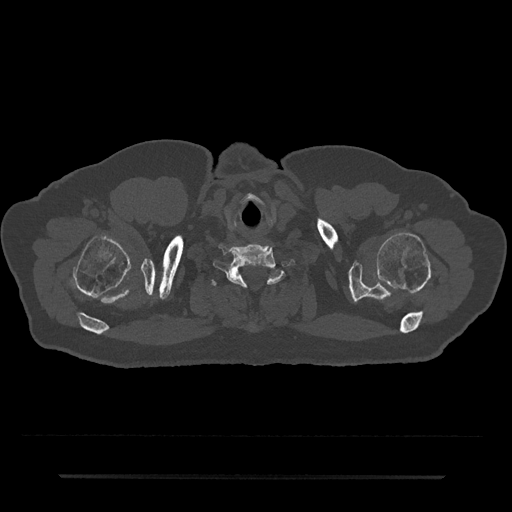
CT including the spine, one axial slice; position 665 of 797 along the scan axis; 120 kVp; bone window (W 1800 / L 400 HU); 0.5 mm slice thickness; 512 × 512 image matrix, field of view 437 × 437 mm. Male patient, age 69 years. Case-level facts recorded for this patient, not image findings: primary cancer: prostate.
Outlined on this slice (semi-automatic segmentation, software-assisted and operator-edited):
- T1 vertebra: bounding box <211,269,281,286> (left, top, right, bottom; pixels)